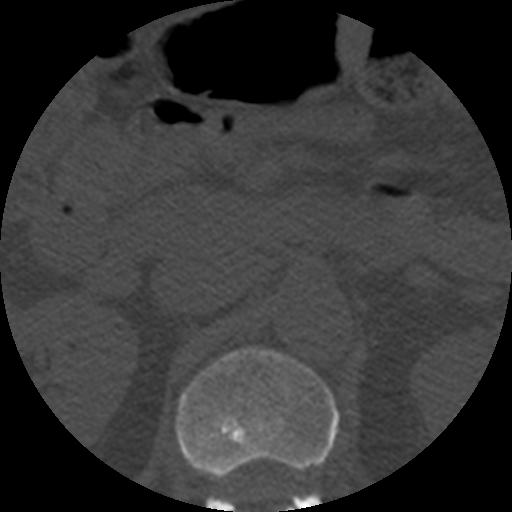
CT including the spine, one axial slice; 120 kVp; bone window (W 1800 / L 400 HU); 1.25 mm slice thickness; 512 × 512 image matrix, field of view 160 × 160 mm. Patient age 57 years. From the clinical record (not read from this slice): primary cancer: prostate.
Annotated regions visible in this slice (semi-automatic segmentation, software-assisted and operator-edited):
- L1 vertebra: bounding box <176,348,339,512> (left, top, right, bottom; pixels)